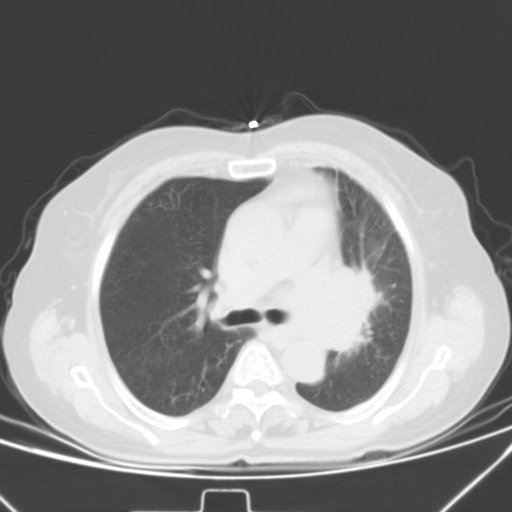
Chest CT, one axial slice. 120 kVp. Lung window (W 1500 / L -600 HU). 512 × 512 image matrix, field of view 331 × 331 mm. Patient: female, 59 years. From the clinical record (not read from this slice): clinical TNM (as recorded): T3 N1 M0; histopathological grade: G3.
Outlined on this slice (bounding box drawn by a radiologist):
- lung tumour (recorded histology: small cell carcinoma): box from (x=334, y=257) to (x=379, y=365) px